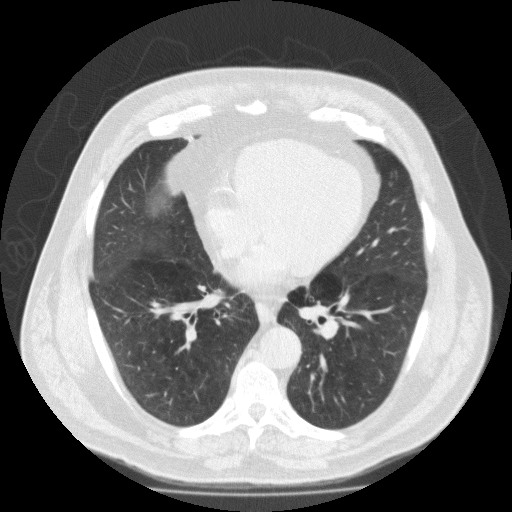
Low-dose screening chest CT, one axial slice. Position 86 of 188 along the scan axis. Reconstruction kernel FC10. 120 kVp. Lung window (W 1500 / L -600 HU). 2 mm slice thickness. 512 × 512 image matrix, field of view 420 × 420 mm.
Annotated regions visible in this slice (manually delineated by an expert):
- lesion 1 (tumor, lower lobe of right lung): box from (x=166, y=135) to (x=199, y=196) px